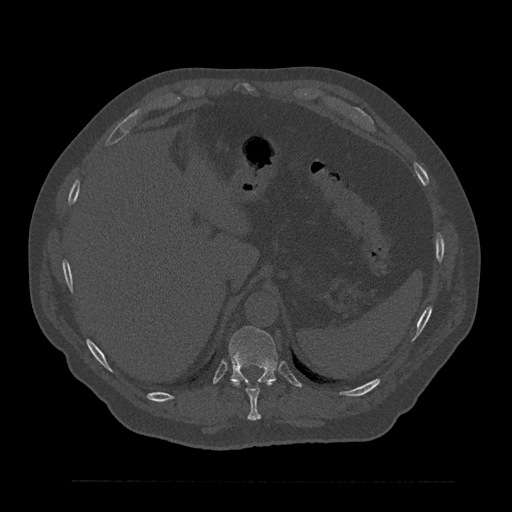
CT including the spine, one axial slice. Slice 320 of 797 in the series (ordered by position). Reconstruction kernel Br40s/3. 120 kVp. Bone window (W 1800 / L 400 HU). 0.5 mm slice thickness. 512 × 512 image matrix, field of view 430 × 430 mm. Male patient, age 61 years. Case-level facts recorded for this patient, not image findings: primary cancer: prostate.
Annotated regions visible in this slice (semi-automatic segmentation, software-assisted and operator-edited):
- T10 vertebra: bounding box <230,379,276,421> (left, top, right, bottom; pixels)
- T11 vertebra: <229,326,278,384>